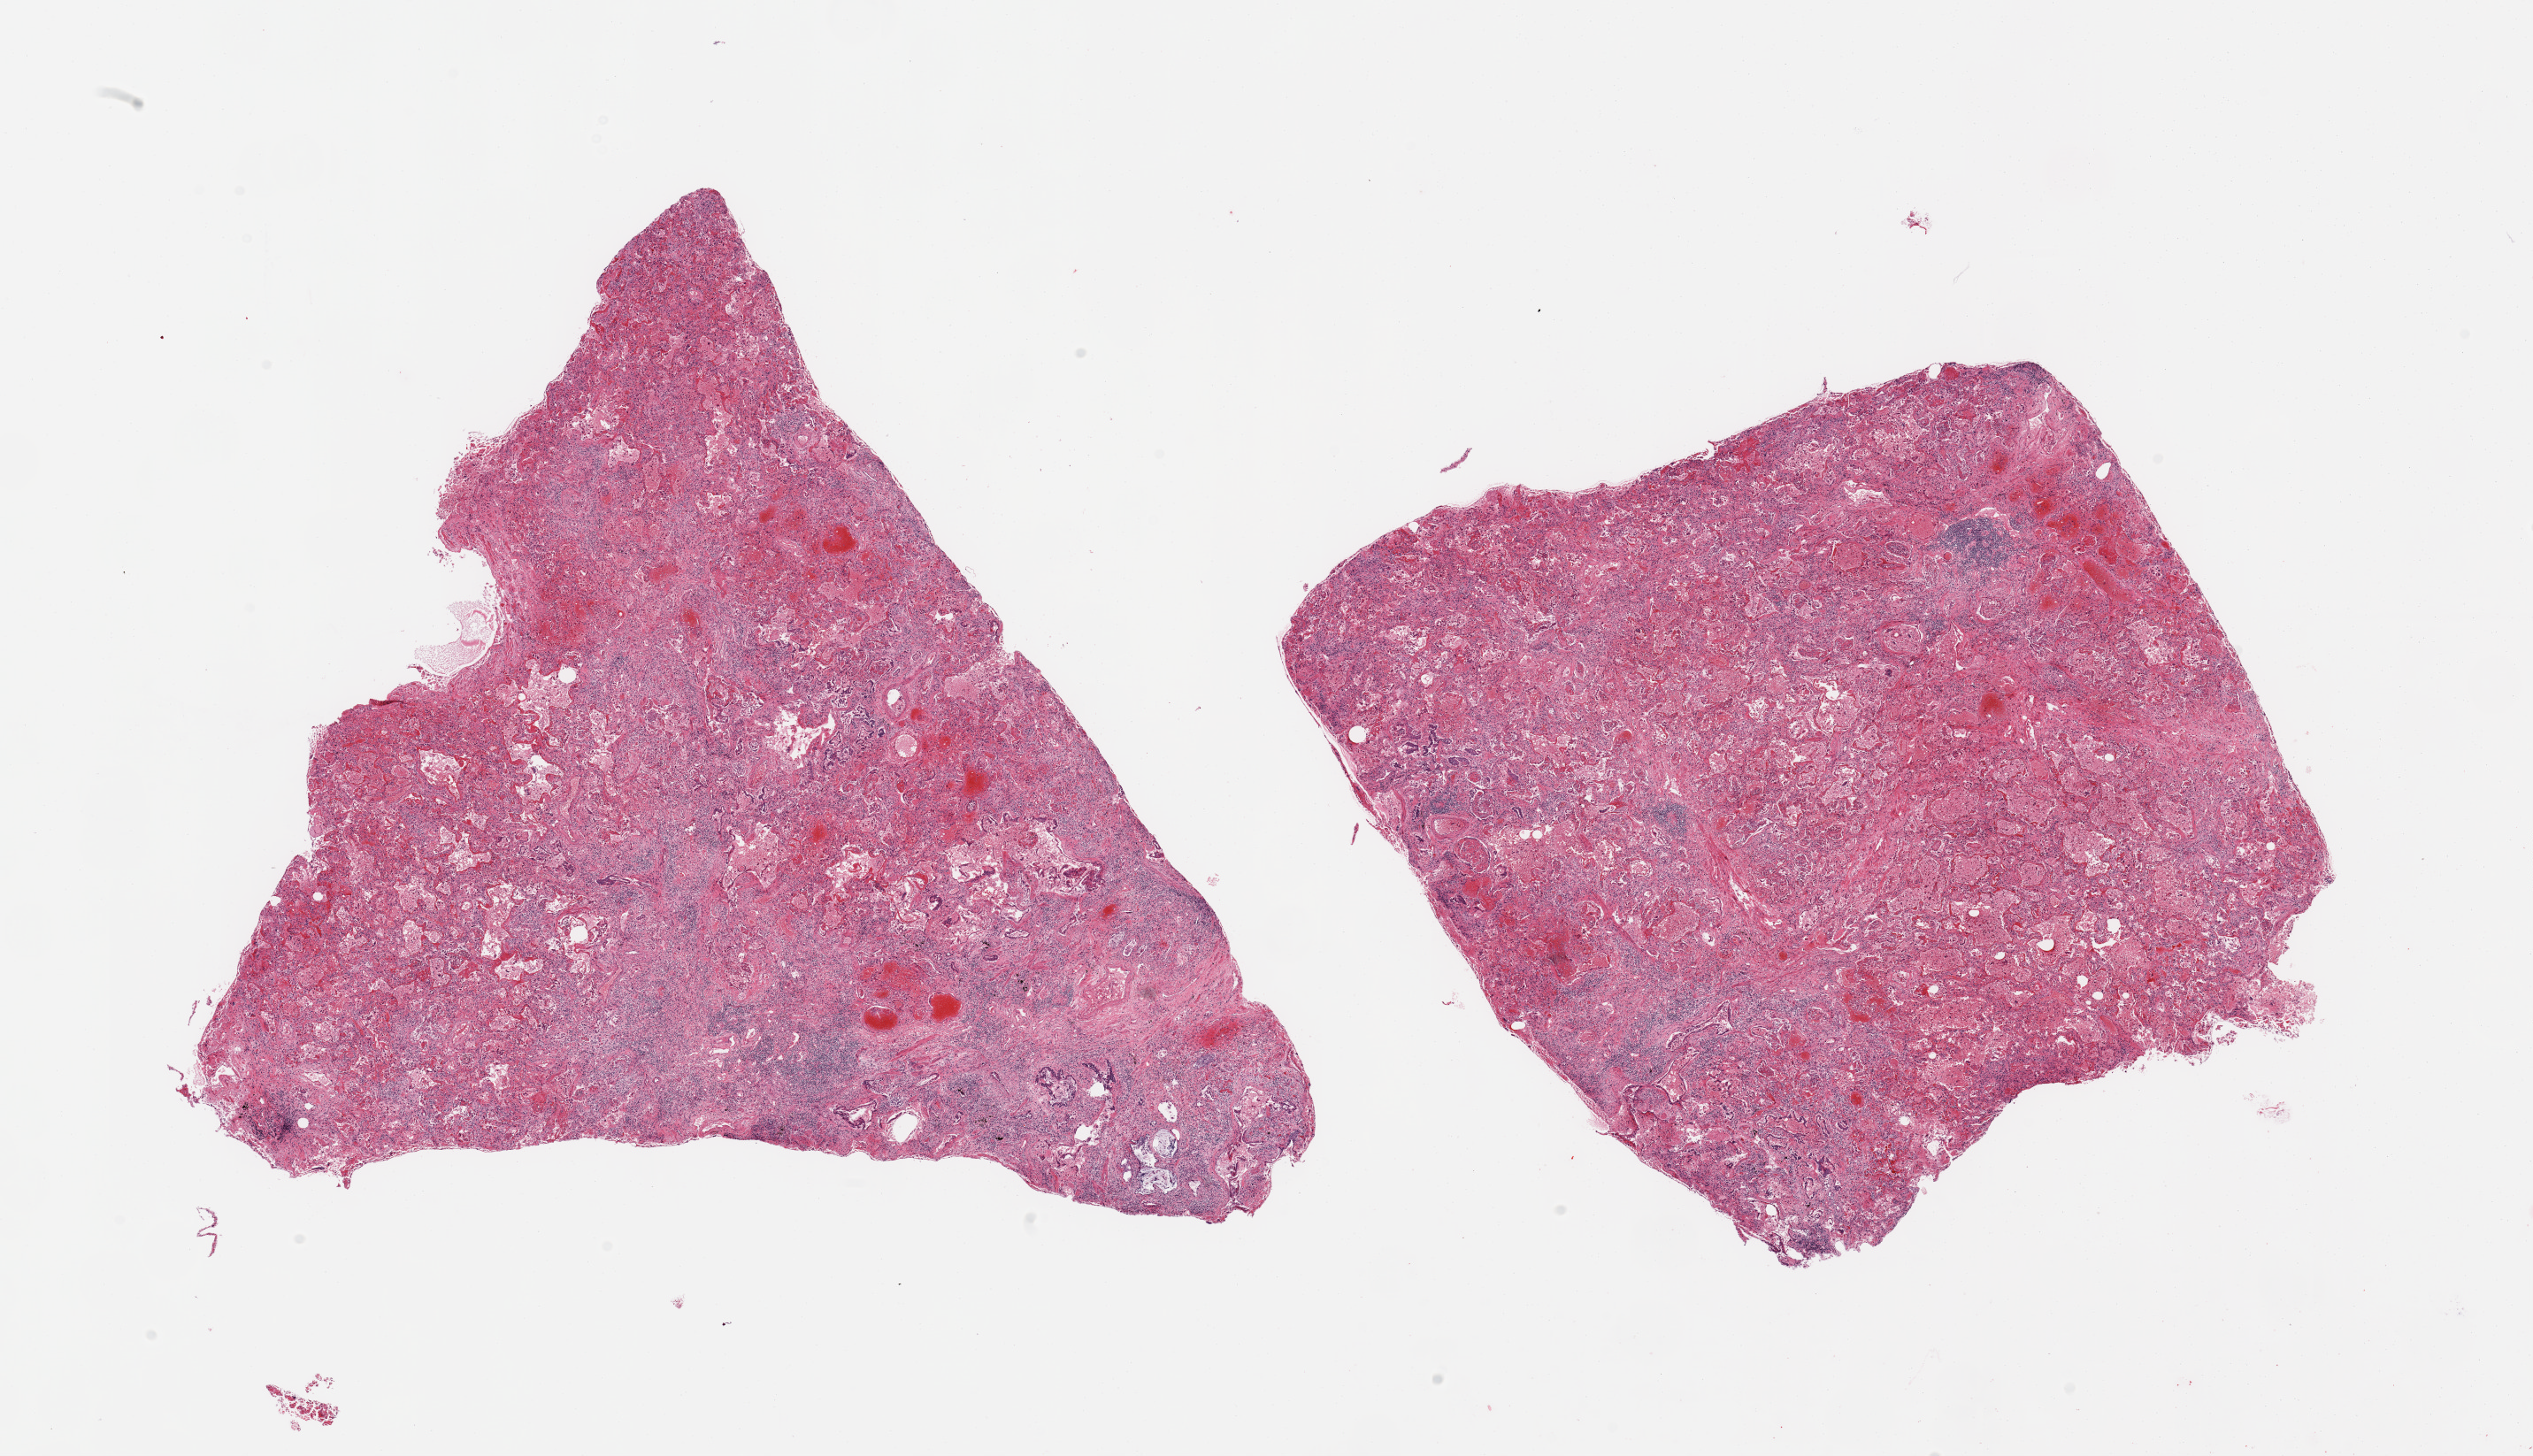
Haematoxylin and eosin whole-slide image, whole scanned area (about 22.6 x 13.0 mm, from a 20x scan) shown as a low-resolution overview. PAXgene-fixed paraffin-embedded (PFPE) section. Sampled site (target tissue): lung. Donor tissue sample. Male donor.
Reviewer comment on this tissue sample: 2 pieces; interstitial fibrosis, chronic inflammation, bronchiectasis.